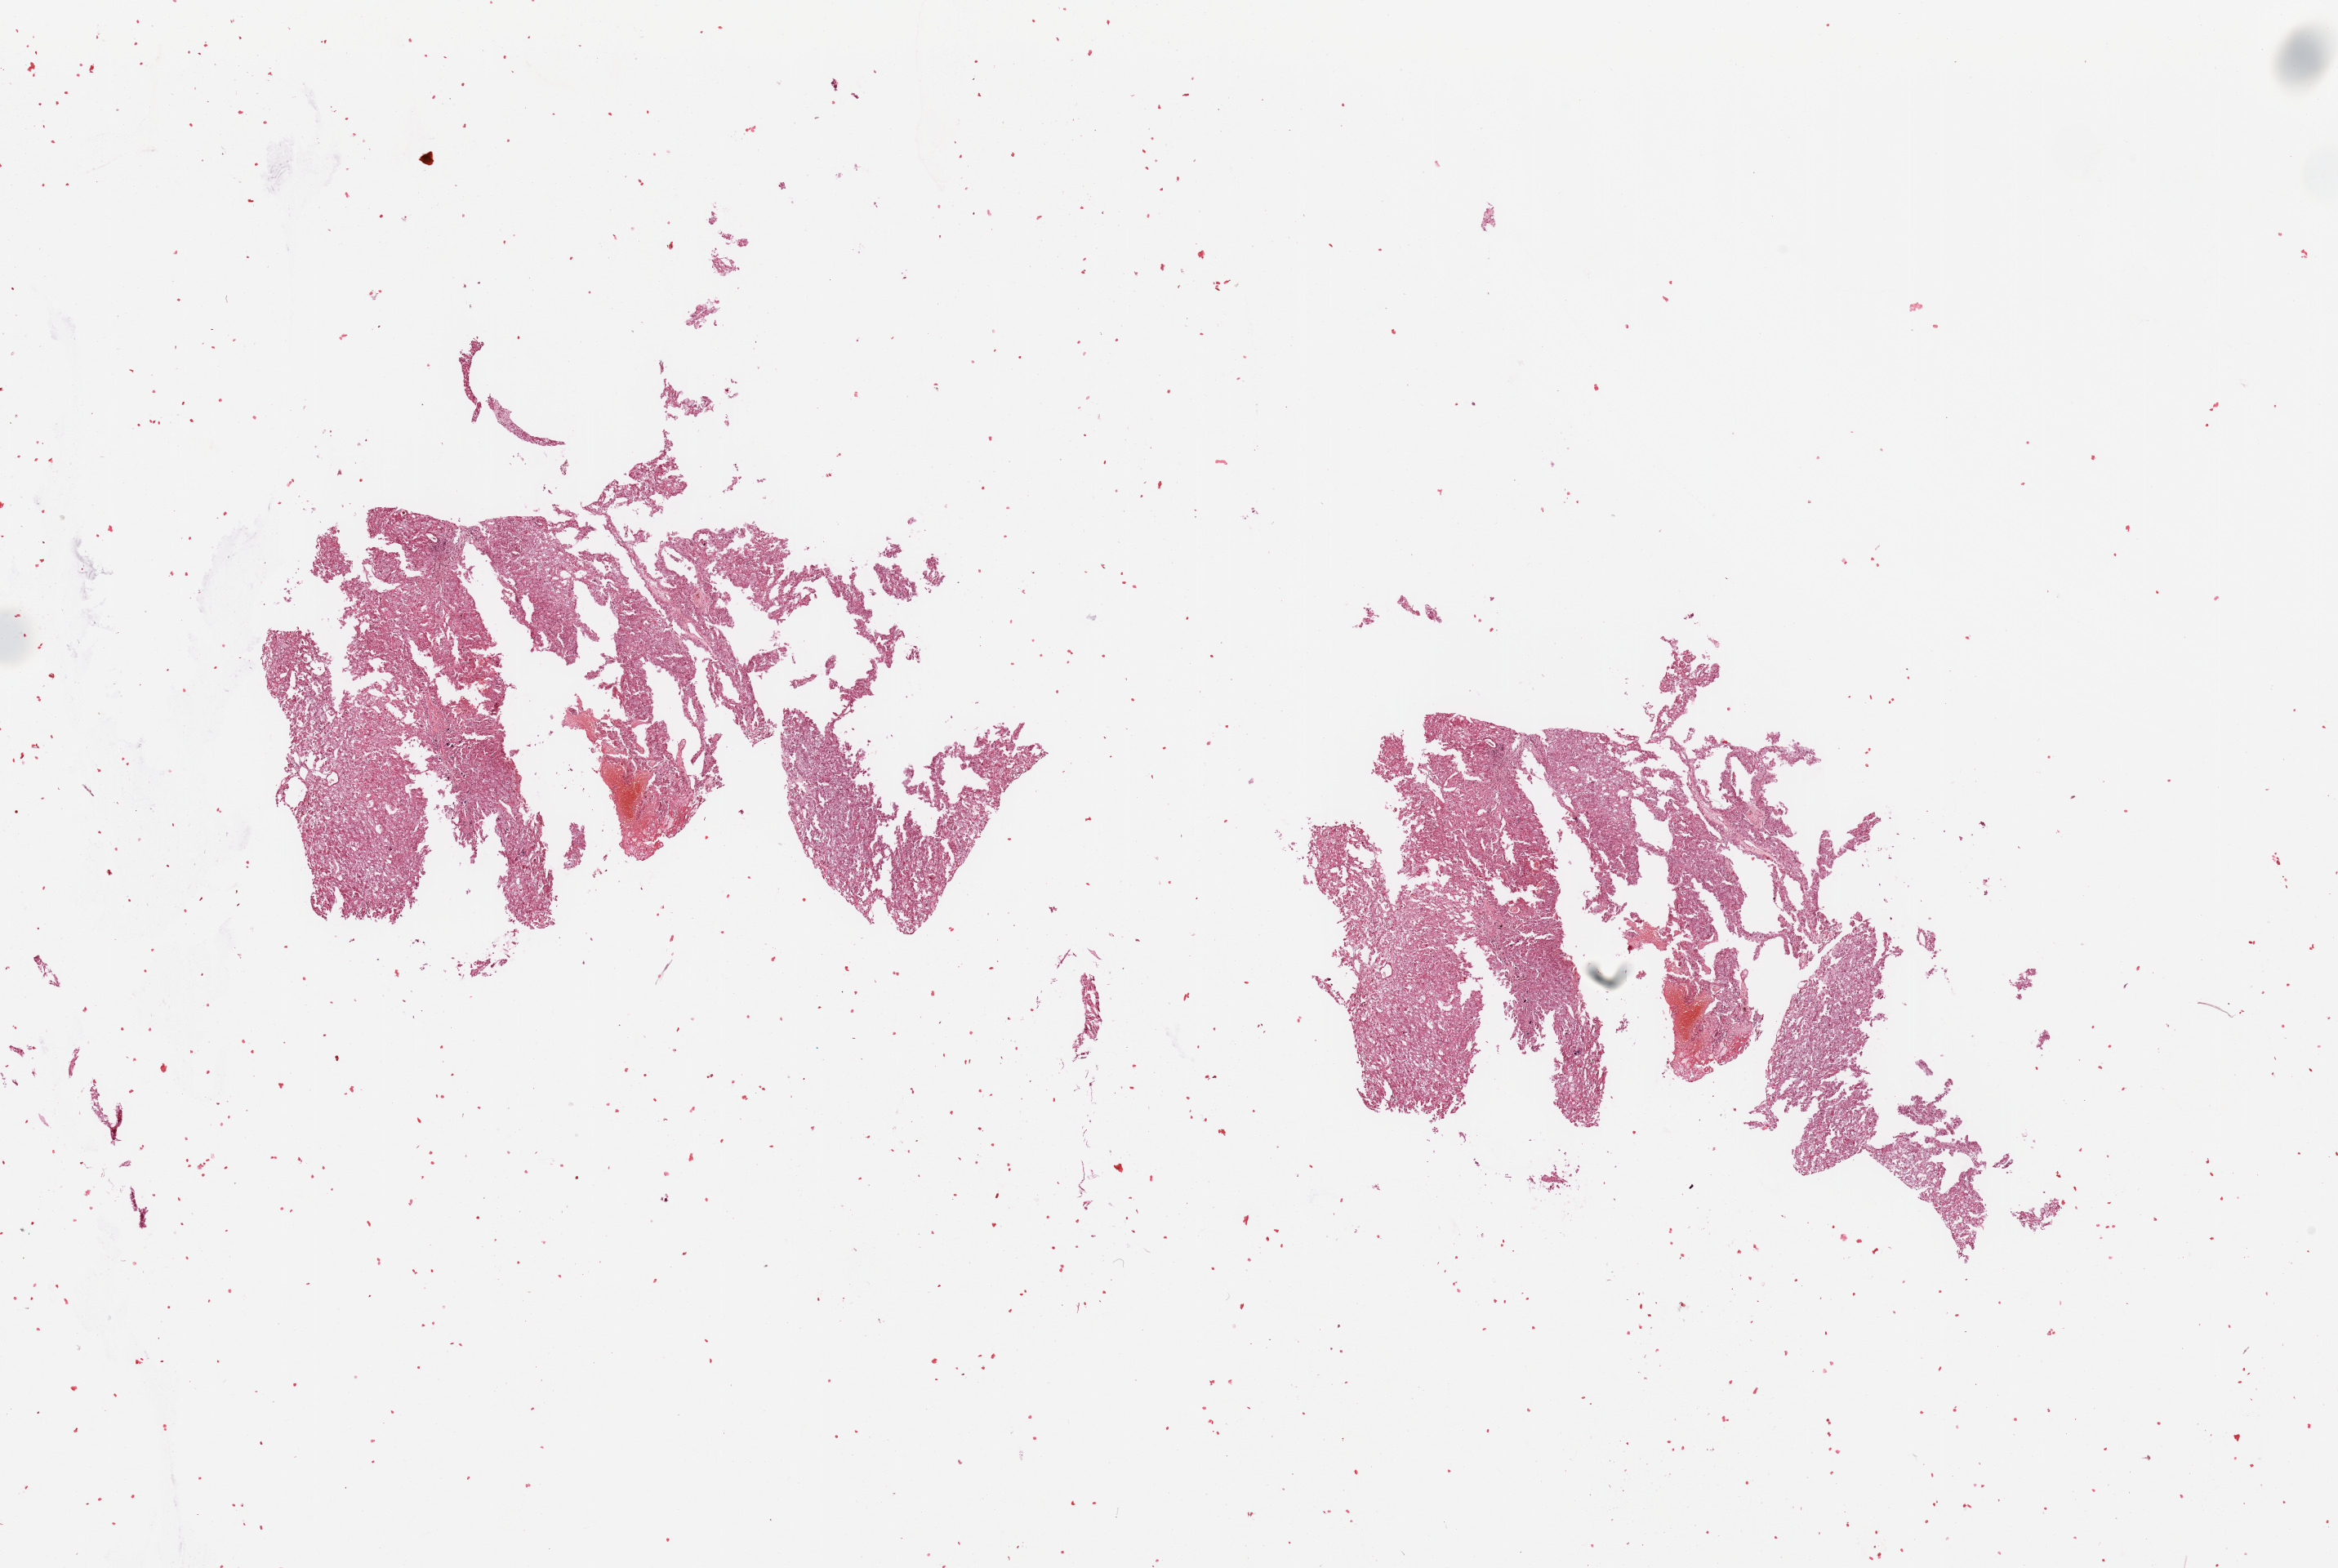
Digitized H&E-stained tissue section (whole slide) — a low-resolution overview of the entire scanned area, about 22.6 x 15.2 mm; tumour tissue sample, sampled site: kidney. 60-year-old female patient. Histologic grade: G2 (moderately differentiated). Composition of this section per pathologist review: tumour nuclei 90%, necrosis 5%.
• primary tumour site (as recorded): middle
• histologic diagnosis: Renal cell carcinoma, NOS
• AJCC pathologic stage: III